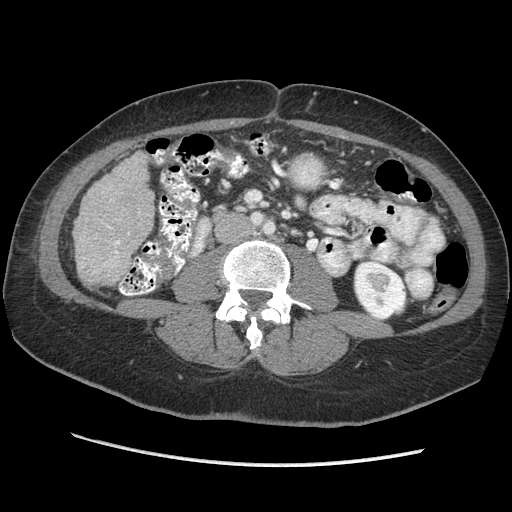
Contrast-enhanced abdominal CT (liver protocol), one axial slice; slice 92 of 170 in the series (ordered by position); 140 kVp; soft-tissue window (W 400 / L 40 HU); 2.5 mm slice thickness; 512 × 512 image matrix, field of view 360 × 360 mm. Case-level facts recorded for this patient, not image findings: diagnosis: hepatocellular carcinoma (patient treated with transarterial chemoembolisation; whether this scan precedes or follows treatment is not stated here); TNM stage (as recorded): Stage-II; Child-Pugh class: A; tumour differentiation: no biopsy; tumour nodularity: multinodular.
Outlined on this slice (semi-automatic segmentation, software-assisted and operator-edited):
- liver parenchyma outside the tumour (the mass and vessels are separate outlines, so this box may not span the whole liver): bounding box <74,152,154,284> (left, top, right, bottom; pixels)
- liver vessels: <105,226,120,264>